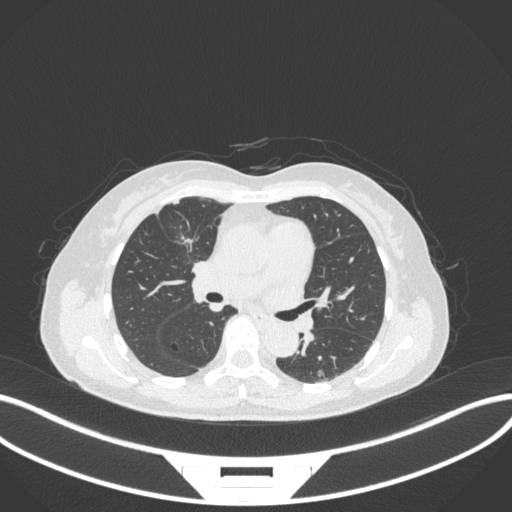
Chest CT, one axial slice. Position 169 of 282 along the scan axis. Reconstruction kernel B31f. 120 kVp. Lung window (W 1500 / L -600 HU). 1 mm slice thickness. 512 × 512 image matrix. Patient: female, 51 years. From the clinical record (not read from this slice): clinical TNM (as recorded): T1c N0 M0.
Outlined on this slice (rectangle marked by the reading radiologist):
- lung tumour (recorded histology: adenocarcinoma): box from (x=177, y=232) to (x=194, y=254) px